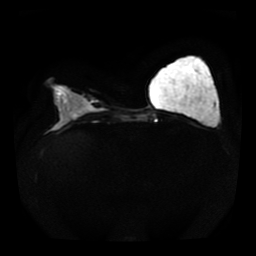
Breast MRI, one axial slice; slice 16 of 41 in the series (ordered by position); diffusion-weighted series; image 2 of 4 stored at this slice position (different b-values; order by instance number); 1.5 T; 5 mm slice thickness; 256 × 256 image matrix, field of view 330 × 330 mm. Female patient.
Outlined on this slice (outlined manually by an expert reader):
- tumour on diffusion-weighted imaging: bounding box <70,112,79,119> (left, top, right, bottom; pixels)